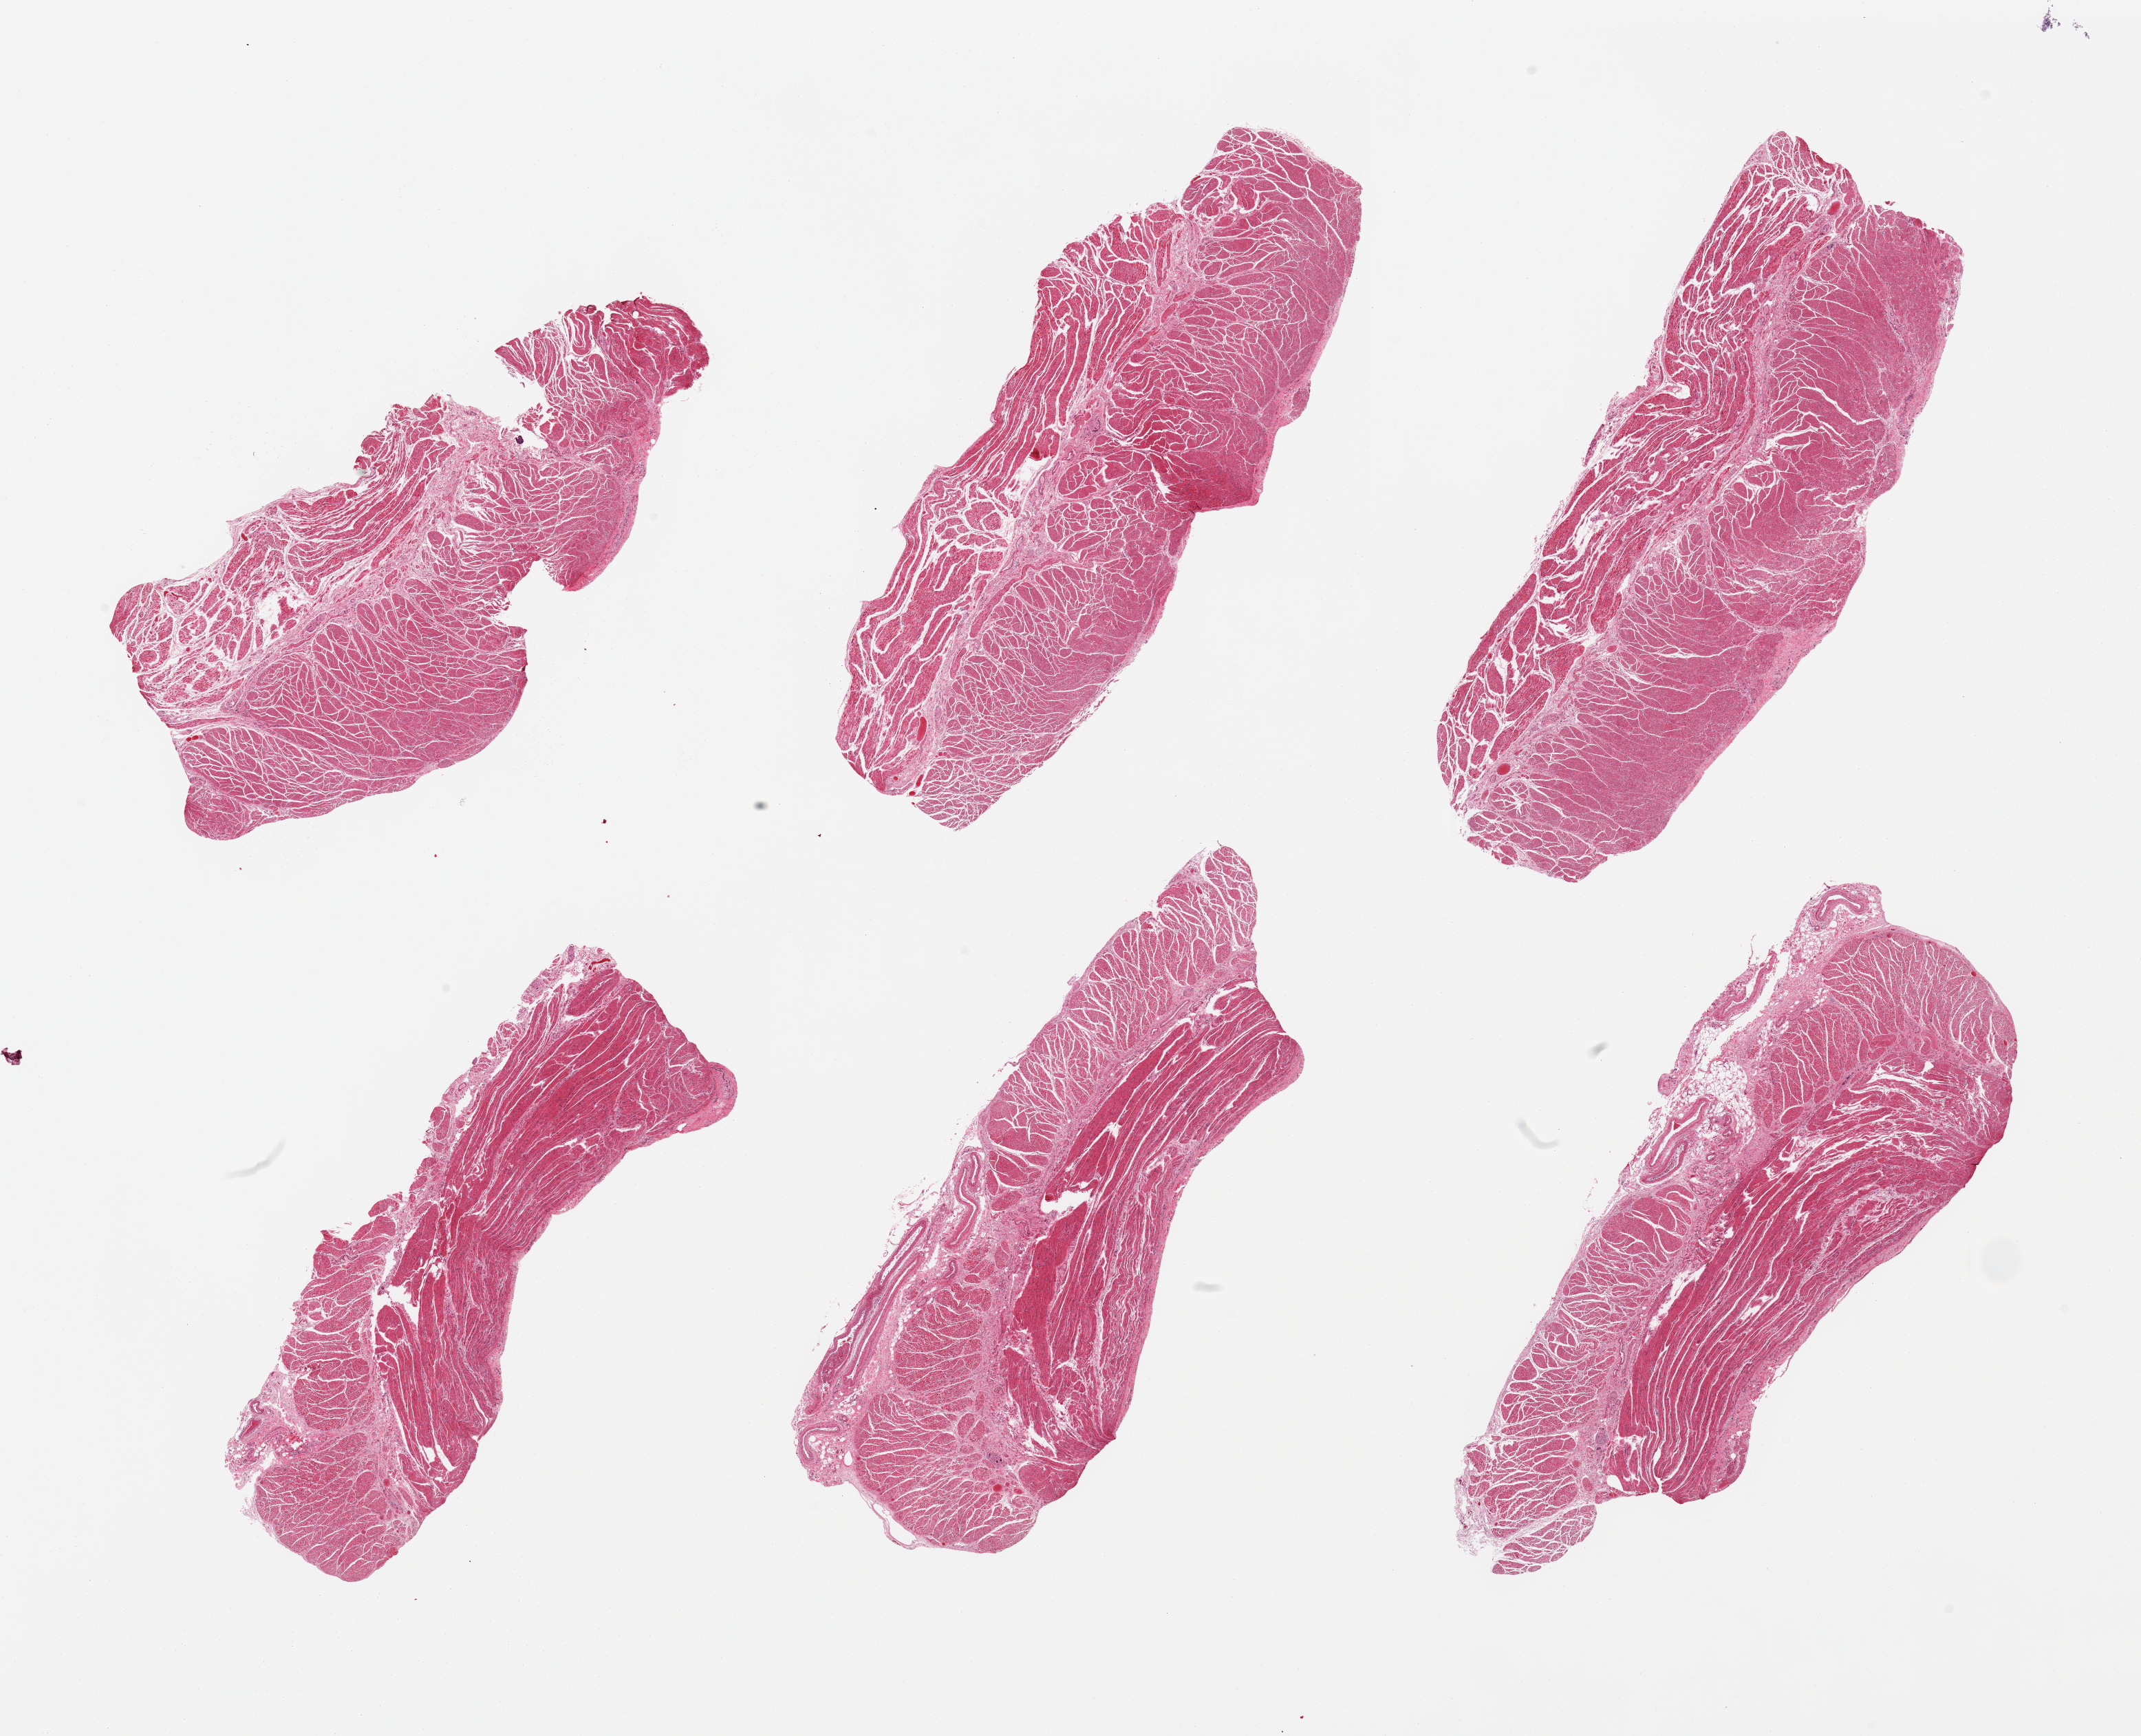
Digitized haematoxylin and eosin-stained section — low-resolution overview of the scanned area, about 24.6 x 20.0 mm (acquisition: 20x scan), PAXgene-fixed, paraffin-embedded tissue, section of gastroesophageal junction (target tissue), donor tissue sample.
- reviewer comment on this tissue sample: 6 pieces; well dissected muscle